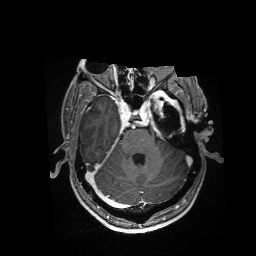
Brain MRI from a brain-tumour surgery series, one axial slice. Slice 114 of 176 in the series (ordered by position). T1-weighted post-contrast. 256 × 256 image matrix, field of view 256 × 256 mm. Case-level facts recorded for this patient, not image findings: histopathology: Glioblastoma; WHO grade: 4; IDH mutation: no.
Structures marked on this image (manually delineated by an expert):
- residual tumour: bounding box (x1, y1, x2, y2) in pixels: (153, 91, 181, 113)